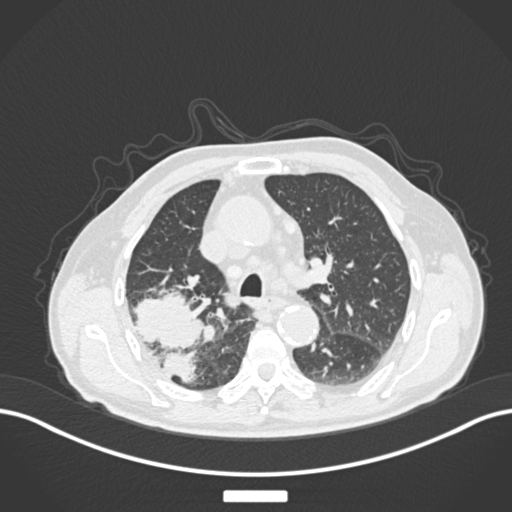
Chest CT, one axial slice. Slice 124 of 201 in the series (ordered by position). Reconstruction kernel B30f. 120 kVp. Lung window (W 1500 / L -600 HU). 512 × 512 image matrix. Male patient, age 72 years. Case-level facts recorded for this patient, not image findings: clinical TNM (as recorded): T3 N2 M0.
Annotated regions visible in this slice (bounding box drawn by a radiologist):
- lung tumour (recorded histology: adenocarcinoma): bounding box <131,287,209,390> (left, top, right, bottom; pixels)